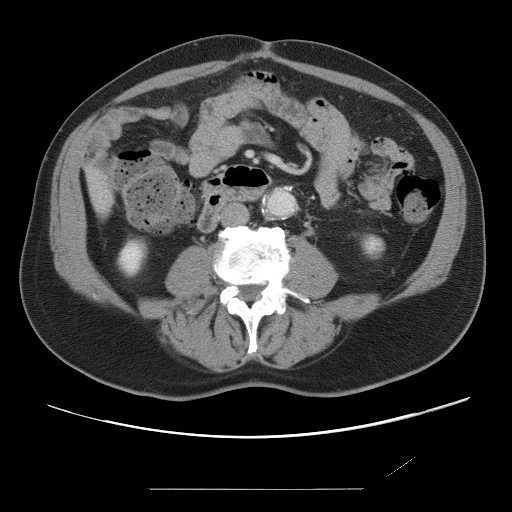
Contrast-enhanced abdominal CT, one axial slice. Slice 8 of 87 in the series (ordered by position). Intravenous contrast given. Soft-tissue window (W 400 / L 40 HU). 5 mm slice thickness. 512 × 512 image matrix. Male patient, age 74 years. Case-level facts recorded for this patient, not image findings: diagnosis: colorectal cancer liver metastases, imaged before liver resection; multiple liver metastases: yes; largest metastasis: 1.1 cm; disease in both lobes: no.
Outlined on this slice (outlined manually by an expert reader):
- liver: bounding box (x1, y1, x2, y2) in pixels: (90, 174, 112, 212)
- planned liver remnant (the part of the liver to remain after resection): (90, 174, 111, 213)